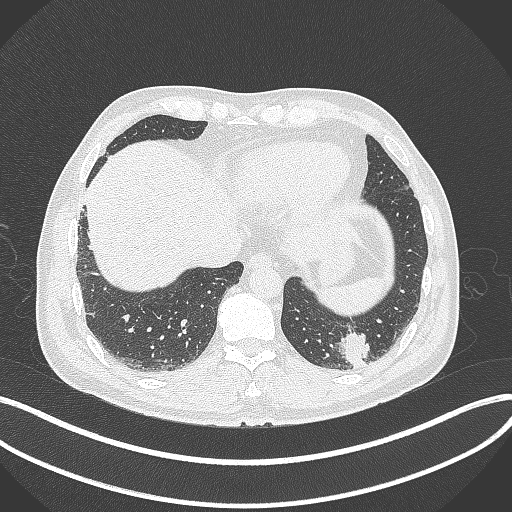
Chest CT, one axial slice; position 60 of 300 along the scan axis; lung window (W 1500 / L -600 HU); 1 mm slice thickness; 512 × 512 image matrix. Male patient, age 54 years. Case-level facts recorded for this patient, not image findings: clinical TNM (as recorded): T1c N0 M1; histopathological grade: G3.
Annotated regions visible in this slice (bounding box drawn by a radiologist):
- lung tumour (recorded histology: adenocarcinoma): box from (x=337, y=329) to (x=373, y=372) px